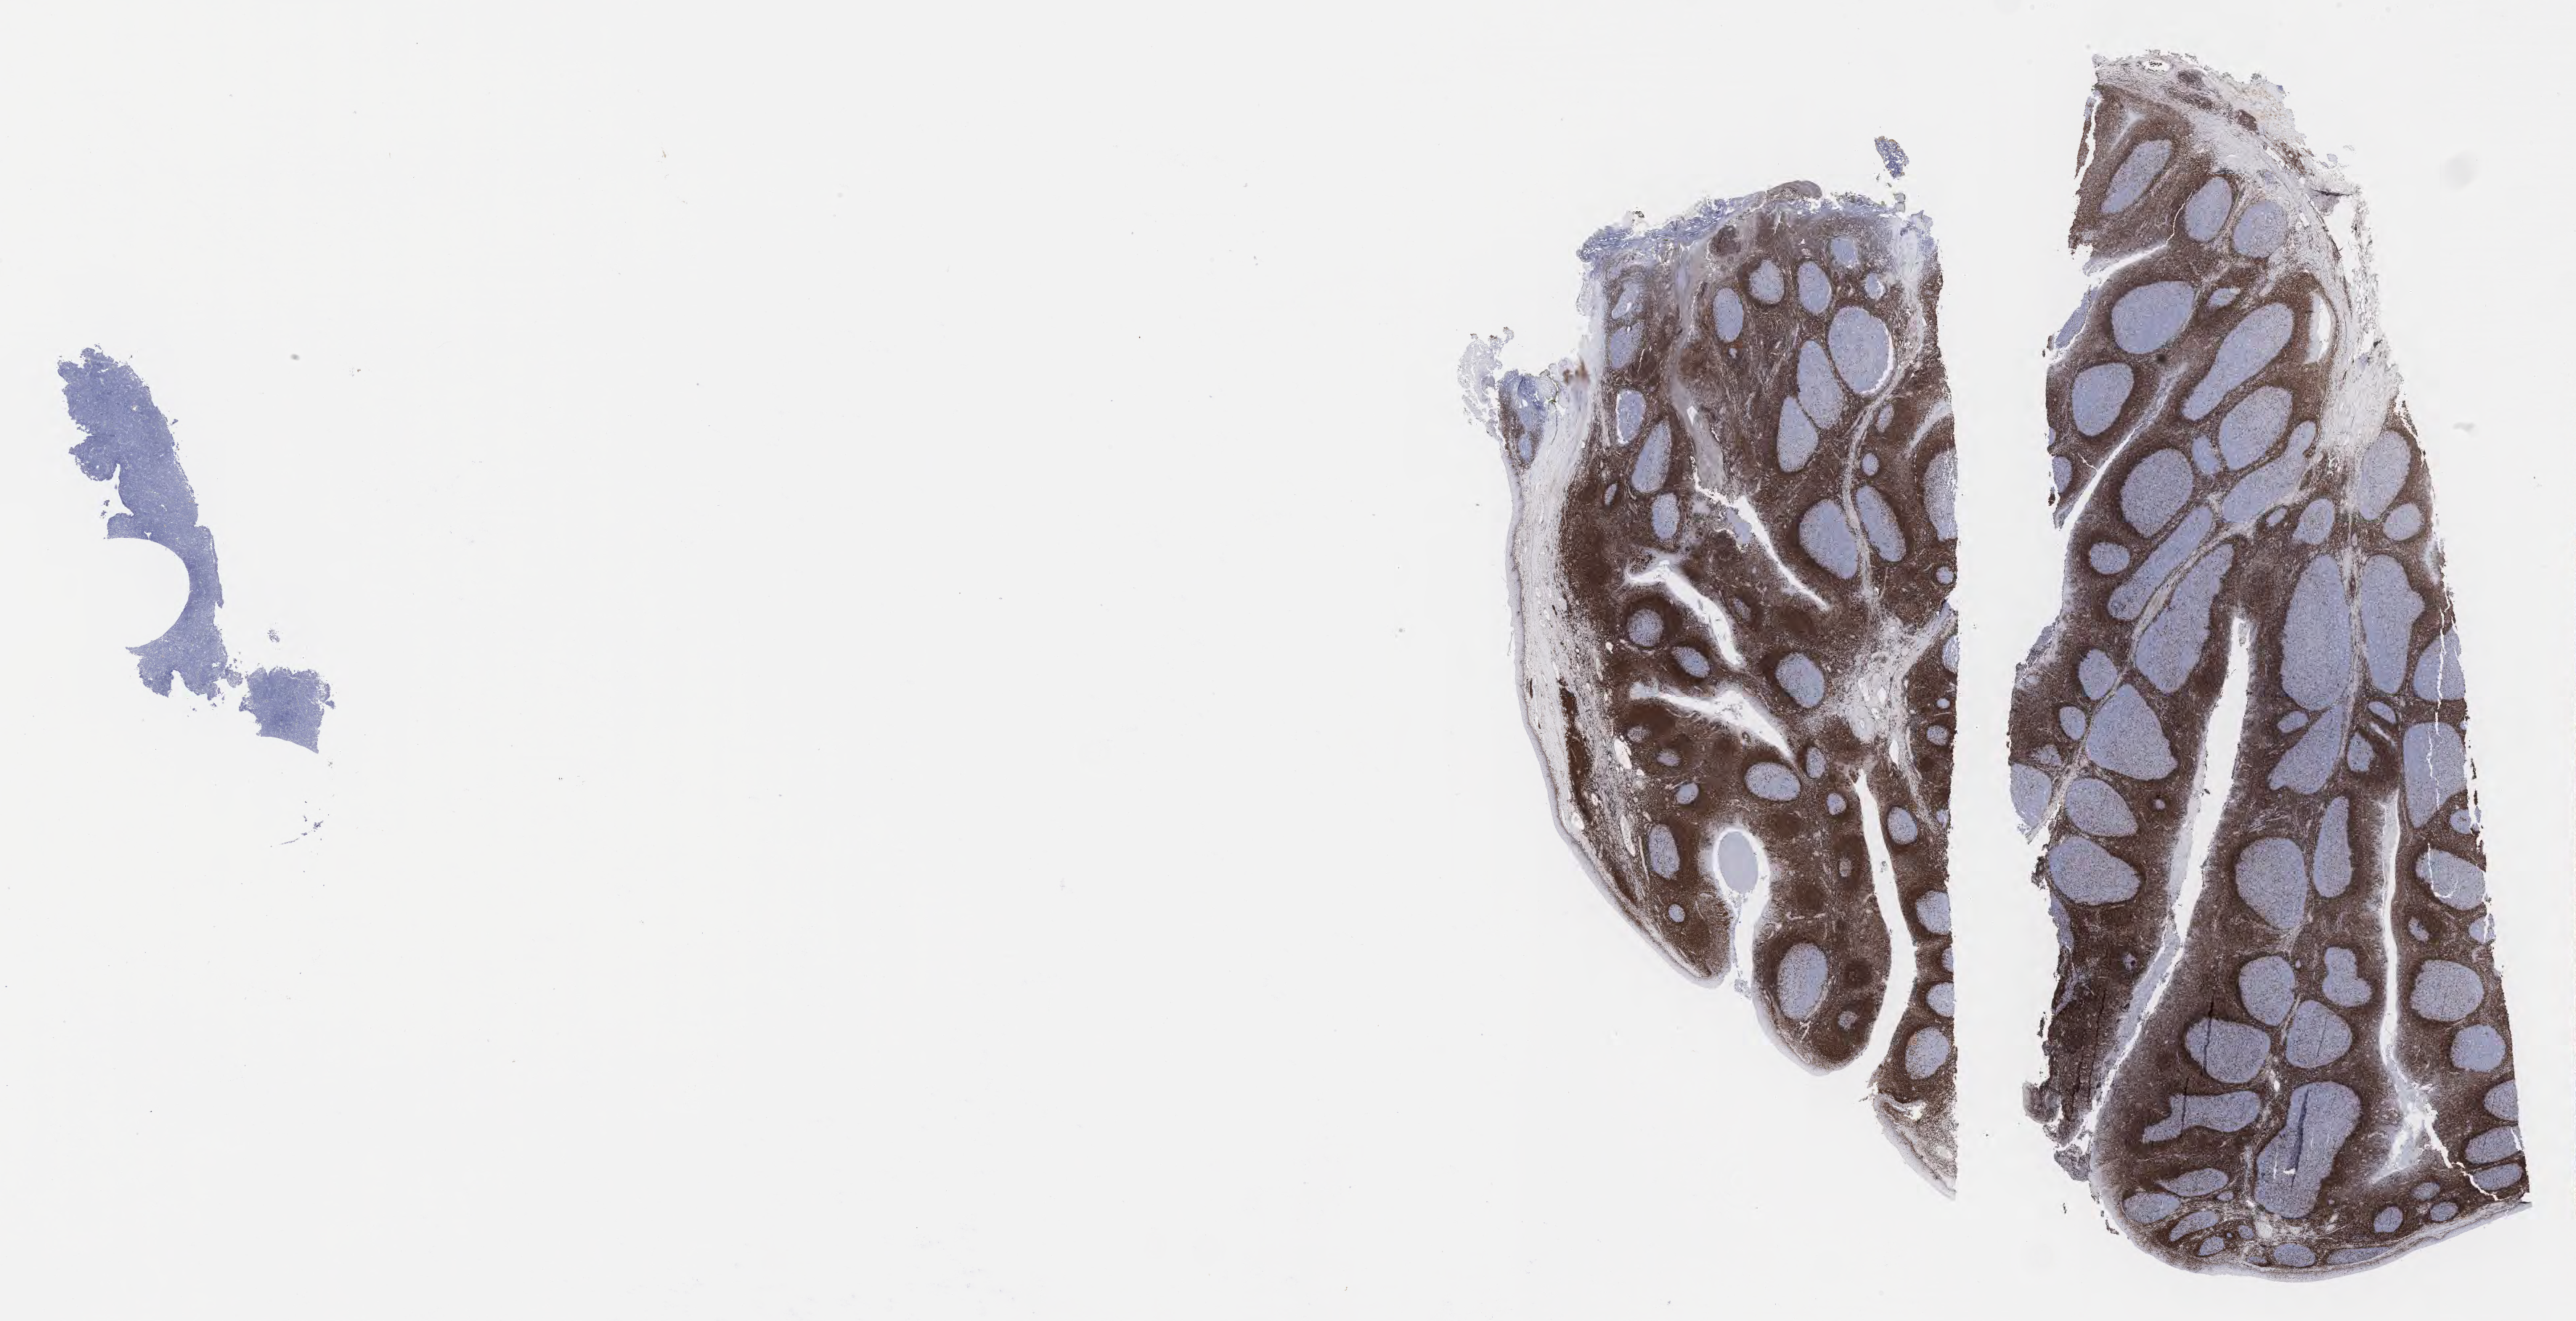
Immunohistochemistry (IHC) whole-slide image stained for BCL2 — whole scanned area (about 28.7 x 14.7 mm) shown as a low-resolution overview. Tumor tissue. Male, age 5 years at initial diagnosis.
* histologic diagnosis: Burkitt lymphoma, NOS